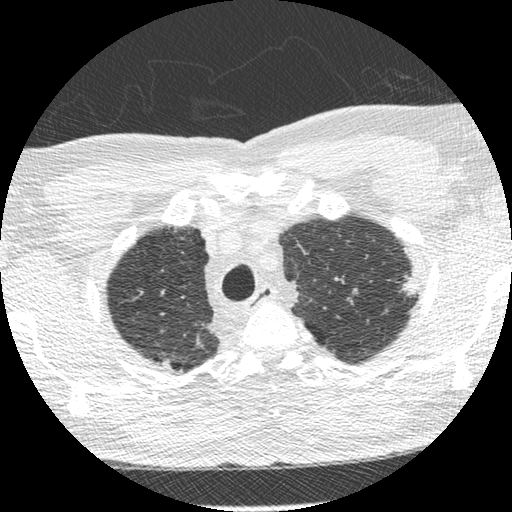
Low-dose screening chest CT, one axial slice. Position 240 of 275 along the scan axis. 120 kVp. Lung window (W 1500 / L -600 HU). 1.25 mm slice thickness. 512 × 512 image matrix, field of view 330 × 330 mm.
Structures marked on this image (outlined manually by an expert reader):
- lesion 1 (tumor, upper lobe of left lung): bounding box [x1, y1, x2, y2] px = [397, 275, 416, 297]